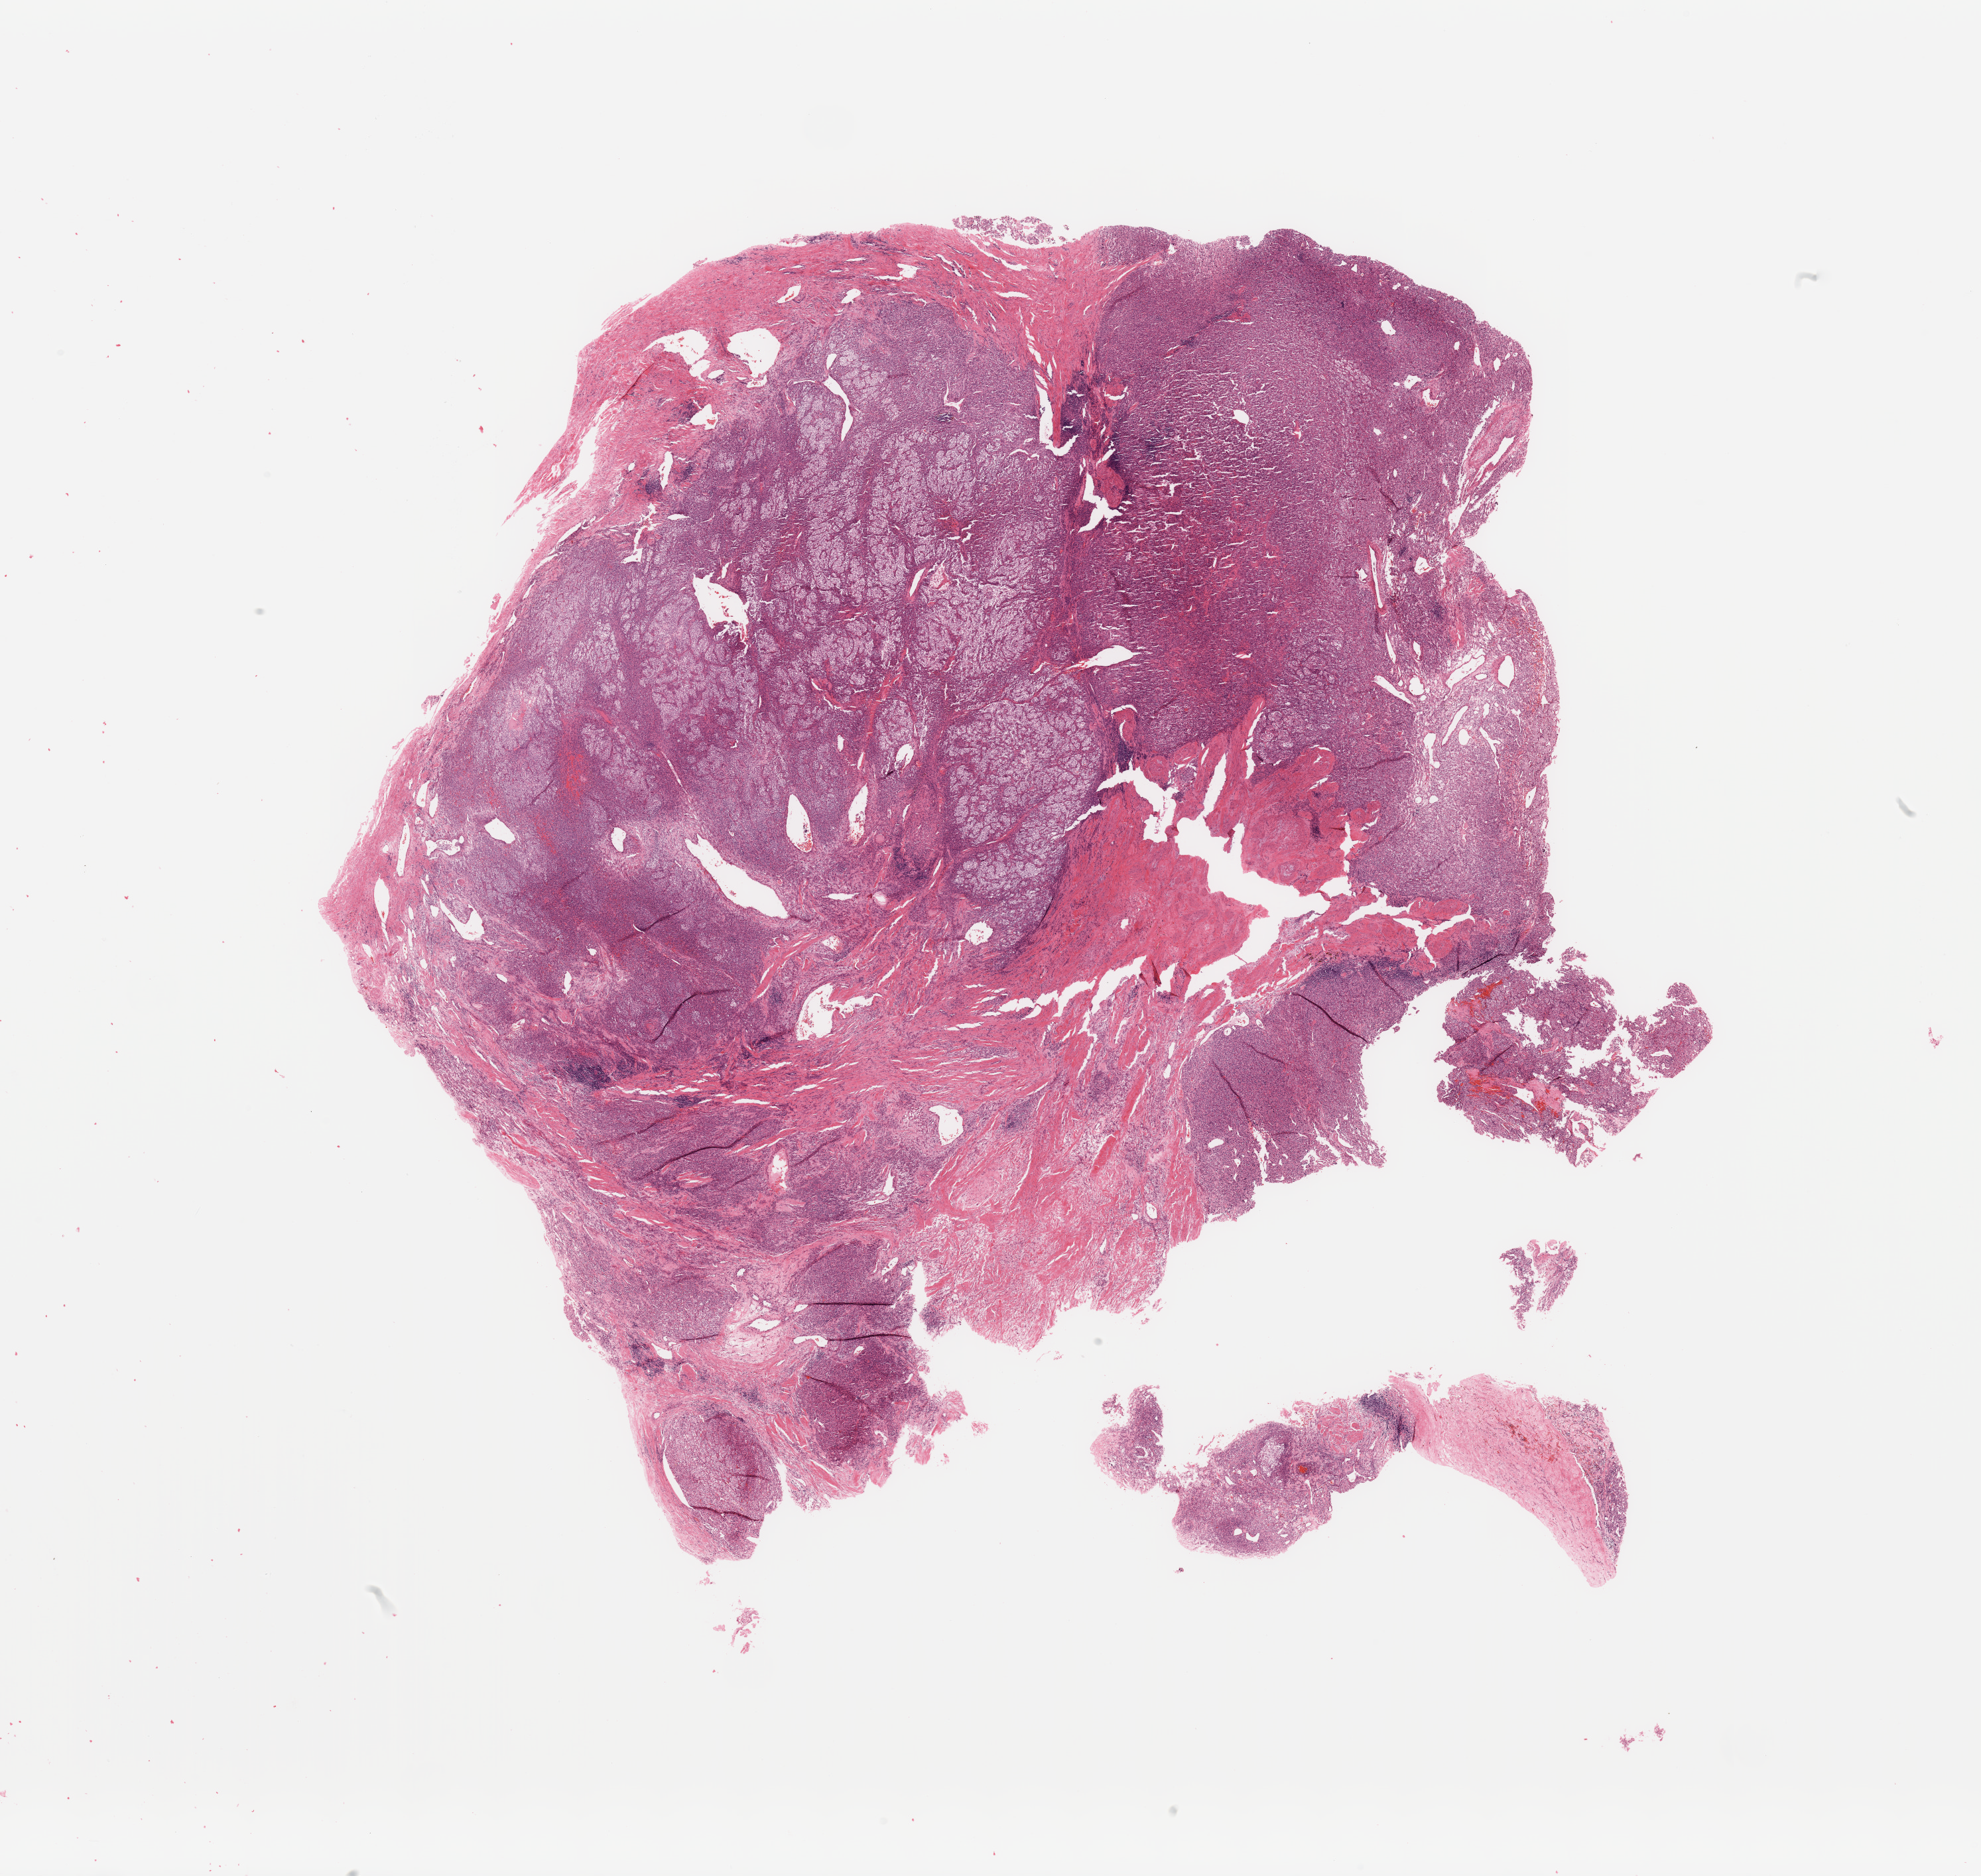
Hematoxylin and eosin (H&E) stained whole-slide image, a low-resolution overview of the entire scanned area, about 23.6 x 22.4 mm. Tumour tissue sample, sampled site: kidney. 52-year-old male patient. Composition of this section per pathologist review: tumour nuclei 80%, necrosis 10%.
Histologic diagnosis: Renal cell carcinoma, NOS.